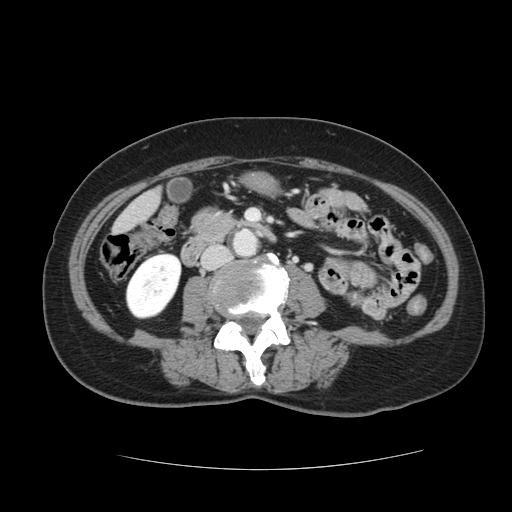
Contrast-enhanced abdominal CT, one axial slice. Slice 16 of 128 in the series (ordered by position). 120 kVp. Soft-tissue window (W 400 / L 40 HU). 2.5 mm slice thickness. 512 × 512 image matrix, field of view 366 × 366 mm. Female patient, age 67 years. Case-level facts recorded for this patient, not image findings: diagnosis: colorectal cancer liver metastases, imaged before liver resection; multiple liver metastases: yes; largest metastasis: 3 cm.
Annotated regions visible in this slice (expert manual segmentation):
- liver: box from (x=115, y=192) to (x=159, y=233) px
- planned liver remnant (the part of the liver to remain after resection): (x=115, y=205)–(x=144, y=233)